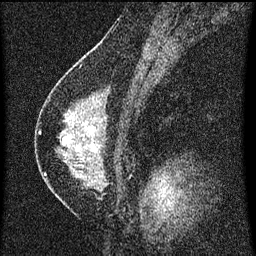
Breast MRI (dynamic contrast-enhanced), one sagittal slice; position 35 of 60 along the scan axis; dynamic contrast-enhanced series, image 2 of 3 at this slice position (ordered by acquisition); 1.5 T; TE 4.2 ms, TR 8 ms; 2 mm slice thickness; 256 × 256 image matrix, field of view 180 × 180 mm. Patient: female, 47 years.
Outlined on this slice (semi-automatic segmentation, software-assisted and operator-edited):
- analysis volume of interest (the breast-tissue region the enhancement analysis was run in; not a lesion): bounding box <42,92,136,199> (left, top, right, bottom; pixels)
- tumour enhancement mask (voxels above the 70 % enhancement threshold inside the analysis volume of interest): <62,136,92,151>